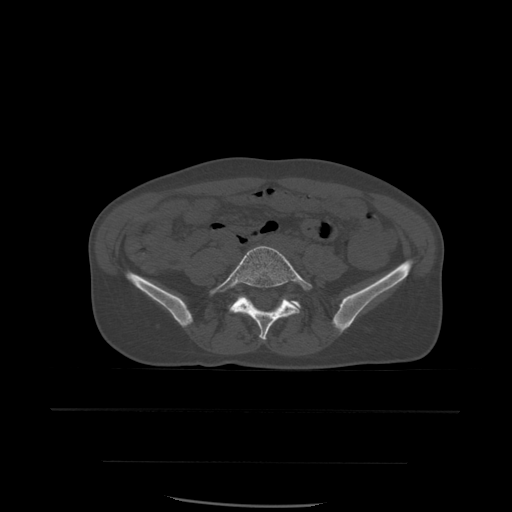
CT including the spine, one axial slice; bone window (W 1800 / L 400 HU); 1.25 mm slice thickness; 512 × 512 image matrix, field of view 392 × 392 mm. Patient age 48 years. From the clinical record (not read from this slice): primary cancer: lung.
Annotated regions visible in this slice (semi-automatic segmentation, software-assisted and operator-edited):
- L5 vertebra: bounding box [x1, y1, x2, y2] px = [209, 246, 313, 341]